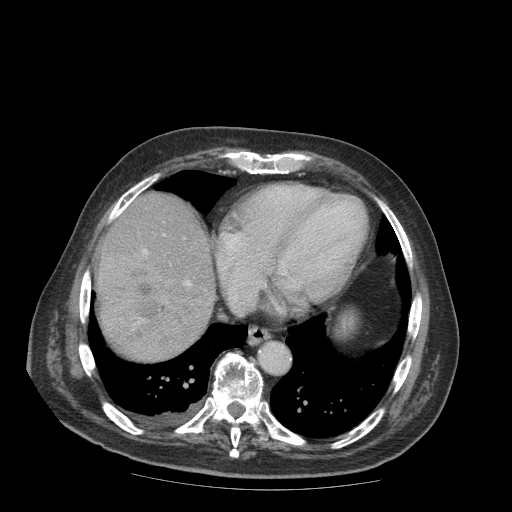
Contrast-enhanced abdominal CT (liver protocol), one axial slice. Position 82 of 99 along the scan axis. 140 kVp. Soft-tissue window (W 400 / L 40 HU). 512 × 512 image matrix. From the clinical record (not read from this slice): diagnosis: hepatocellular carcinoma (patient treated with transarterial chemoembolisation; whether this scan precedes or follows treatment is not stated here); TNM stage (as recorded): Stage-IIIB; Child-Pugh class: A; tumour differentiation: well differentiated; tumour nodularity: multinodular.
Annotated regions visible in this slice (semi-automatically segmented with operator editing):
- liver parenchyma outside the tumour (the mass and vessels are separate outlines, so this box may not span the whole liver): bounding box <96,192,214,325> (left, top, right, bottom; pixels)
- mass: <96,255,210,363>
- liver vessels: <142,234,191,286>